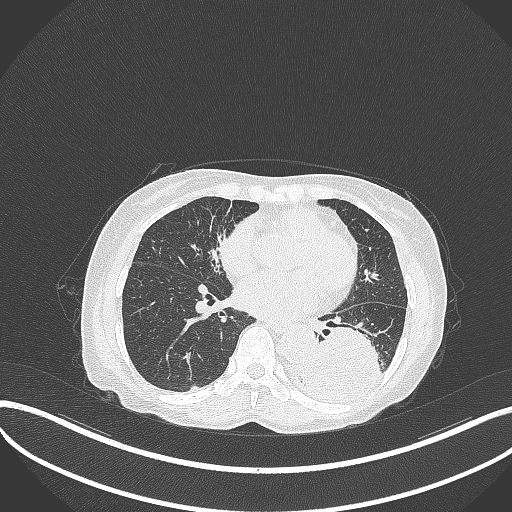
Chest CT, one axial slice; position 132 of 370 along the scan axis; reconstruction kernel B70f; lung window (W 1500 / L -600 HU); 1 mm slice thickness; 512 × 512 image matrix, field of view 400 × 400 mm. Patient: female, 78 years. From the clinical record (not read from this slice): clinical TNM (as recorded): T3 N0 M1.
Structures marked on this image (bounding box drawn by a radiologist):
- lung tumour (recorded histology: squamous cell carcinoma): bounding box (x1, y1, x2, y2) in pixels: (301, 321, 391, 410)